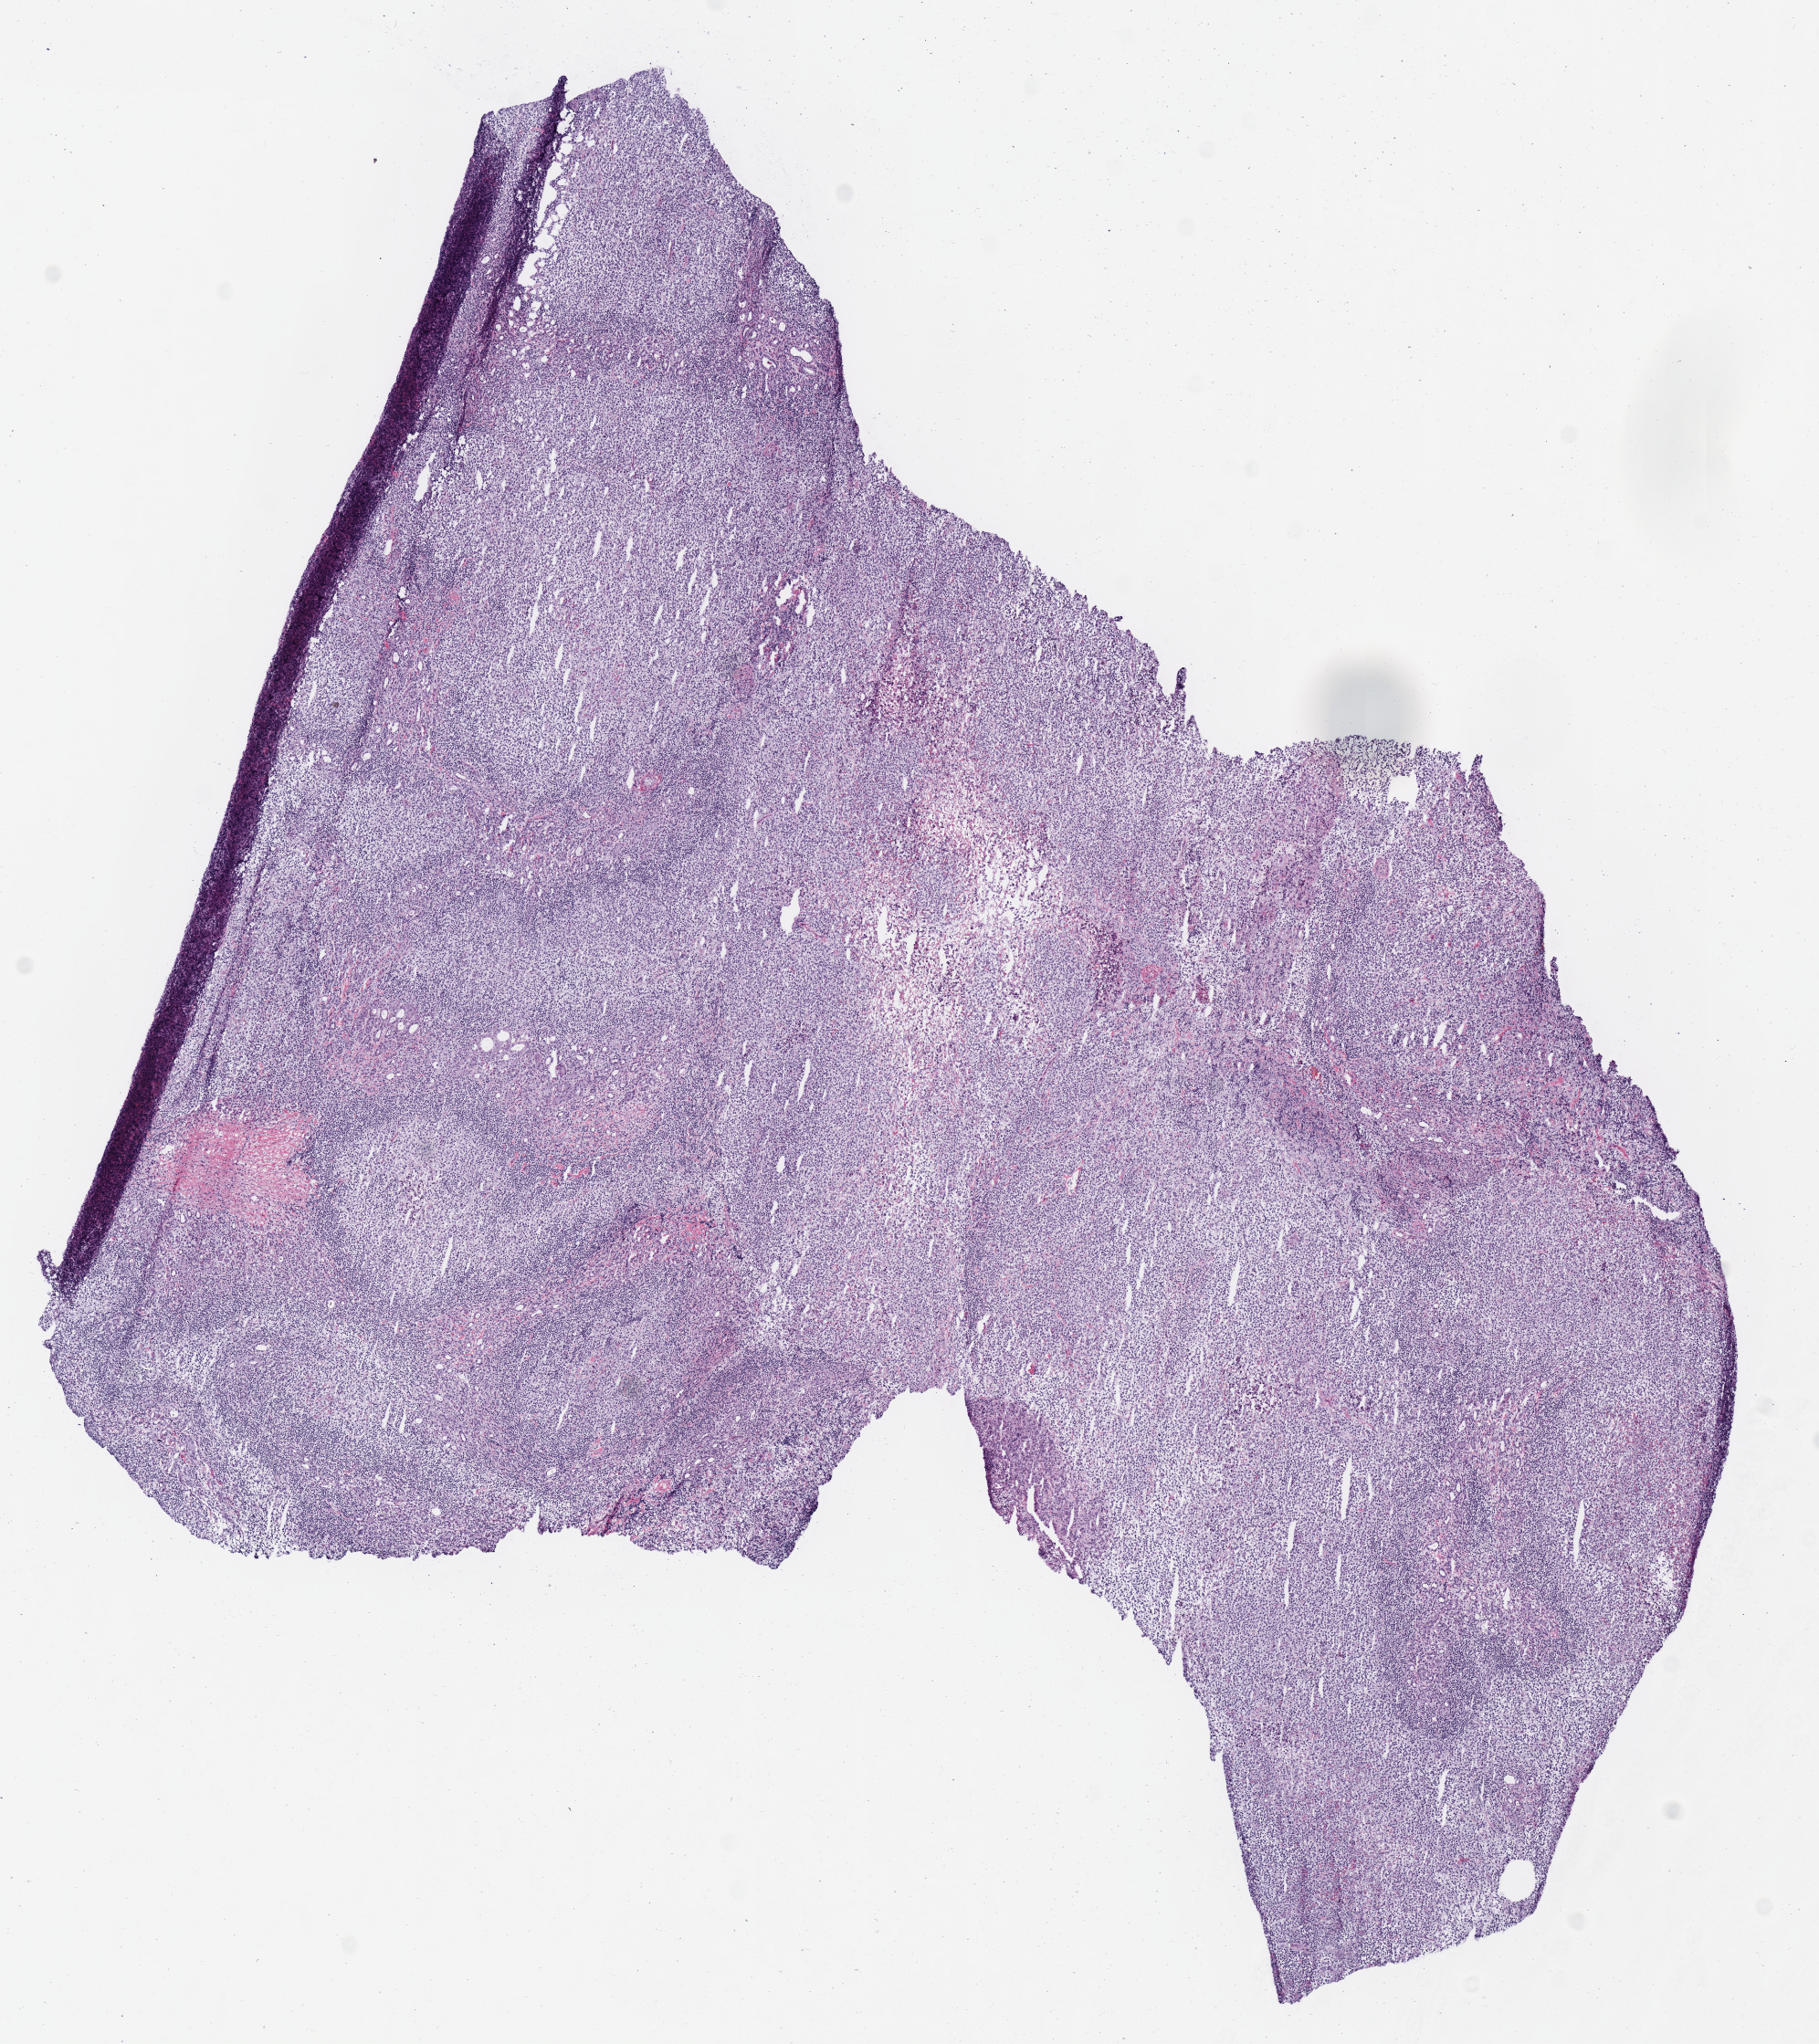
Whole-slide histology image, Hematoxylin and eosin (H&E) stained, a low-resolution overview of the entire scanned area, about 7.8 x 8.8 mm. Frozen section from the bottom of the tissue portion. Lymphoid tissue, primary tumour sample. Patient: female, age at initial diagnosis 60 years. Composition of this section per pathologist review: tumour cells 90%, tumour nuclei 90%.
Histologic diagnosis: Diffuse large B-cell lymphoma, NOS (thyroid gland).